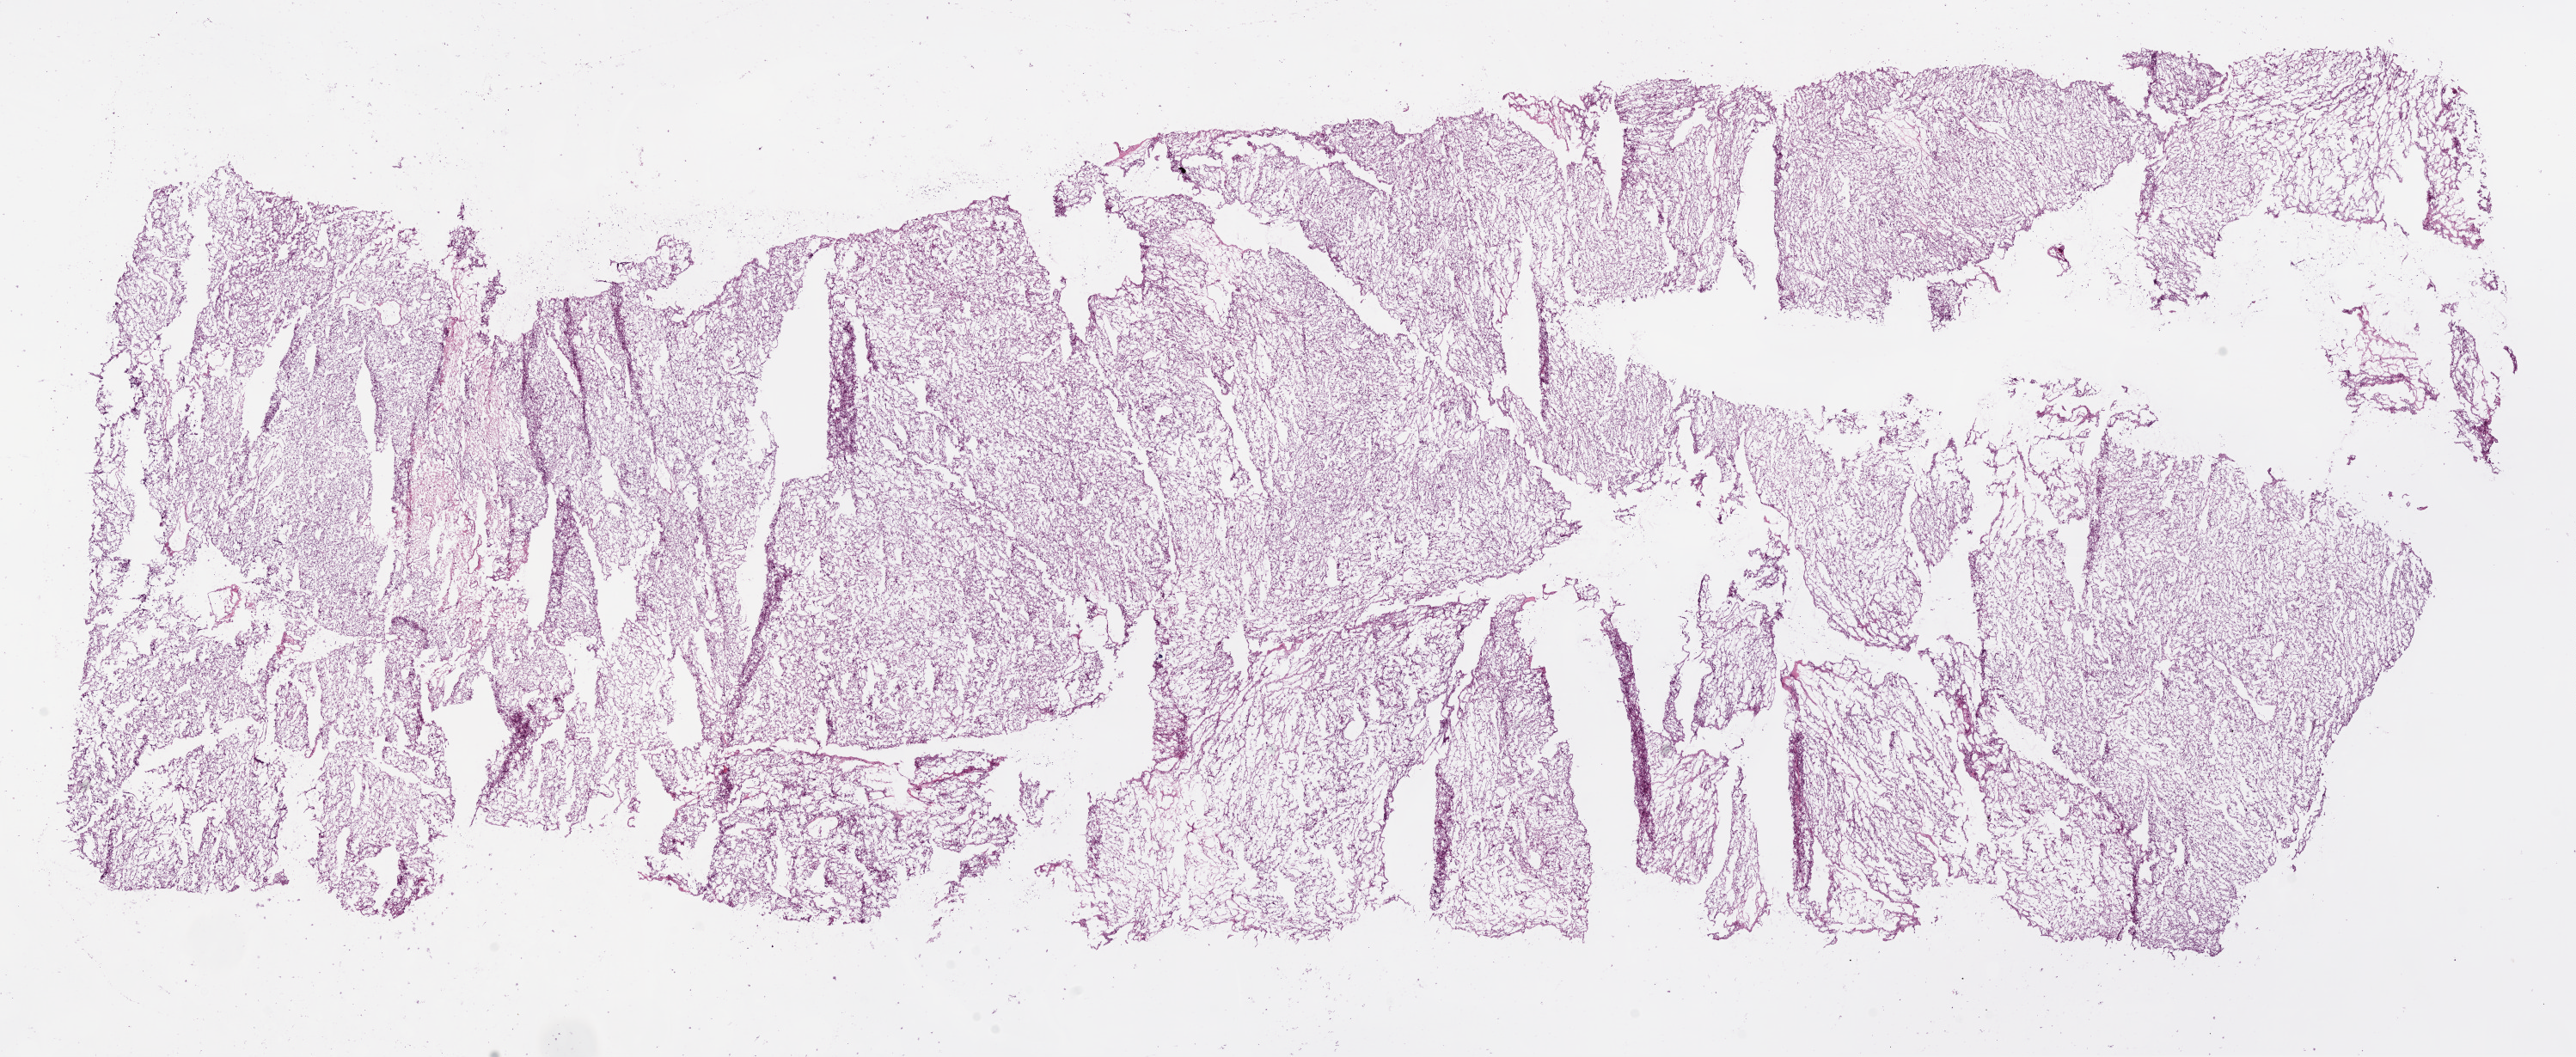
Whole-slide histology image, H&E-stained, shown as a low-resolution overview of the whole scanned area (about 24.2 x 9.9 mm, slide scanned at 20x). Frozen section from the bottom of the tissue portion. Sample: primary tumour, kidney. Male, age 78 years at initial diagnosis. Composition of this section per pathologist review: tumour cells 92%, tumour nuclei 85%.
Pathologic diagnosis: Clear cell adenocarcinoma, NOS.